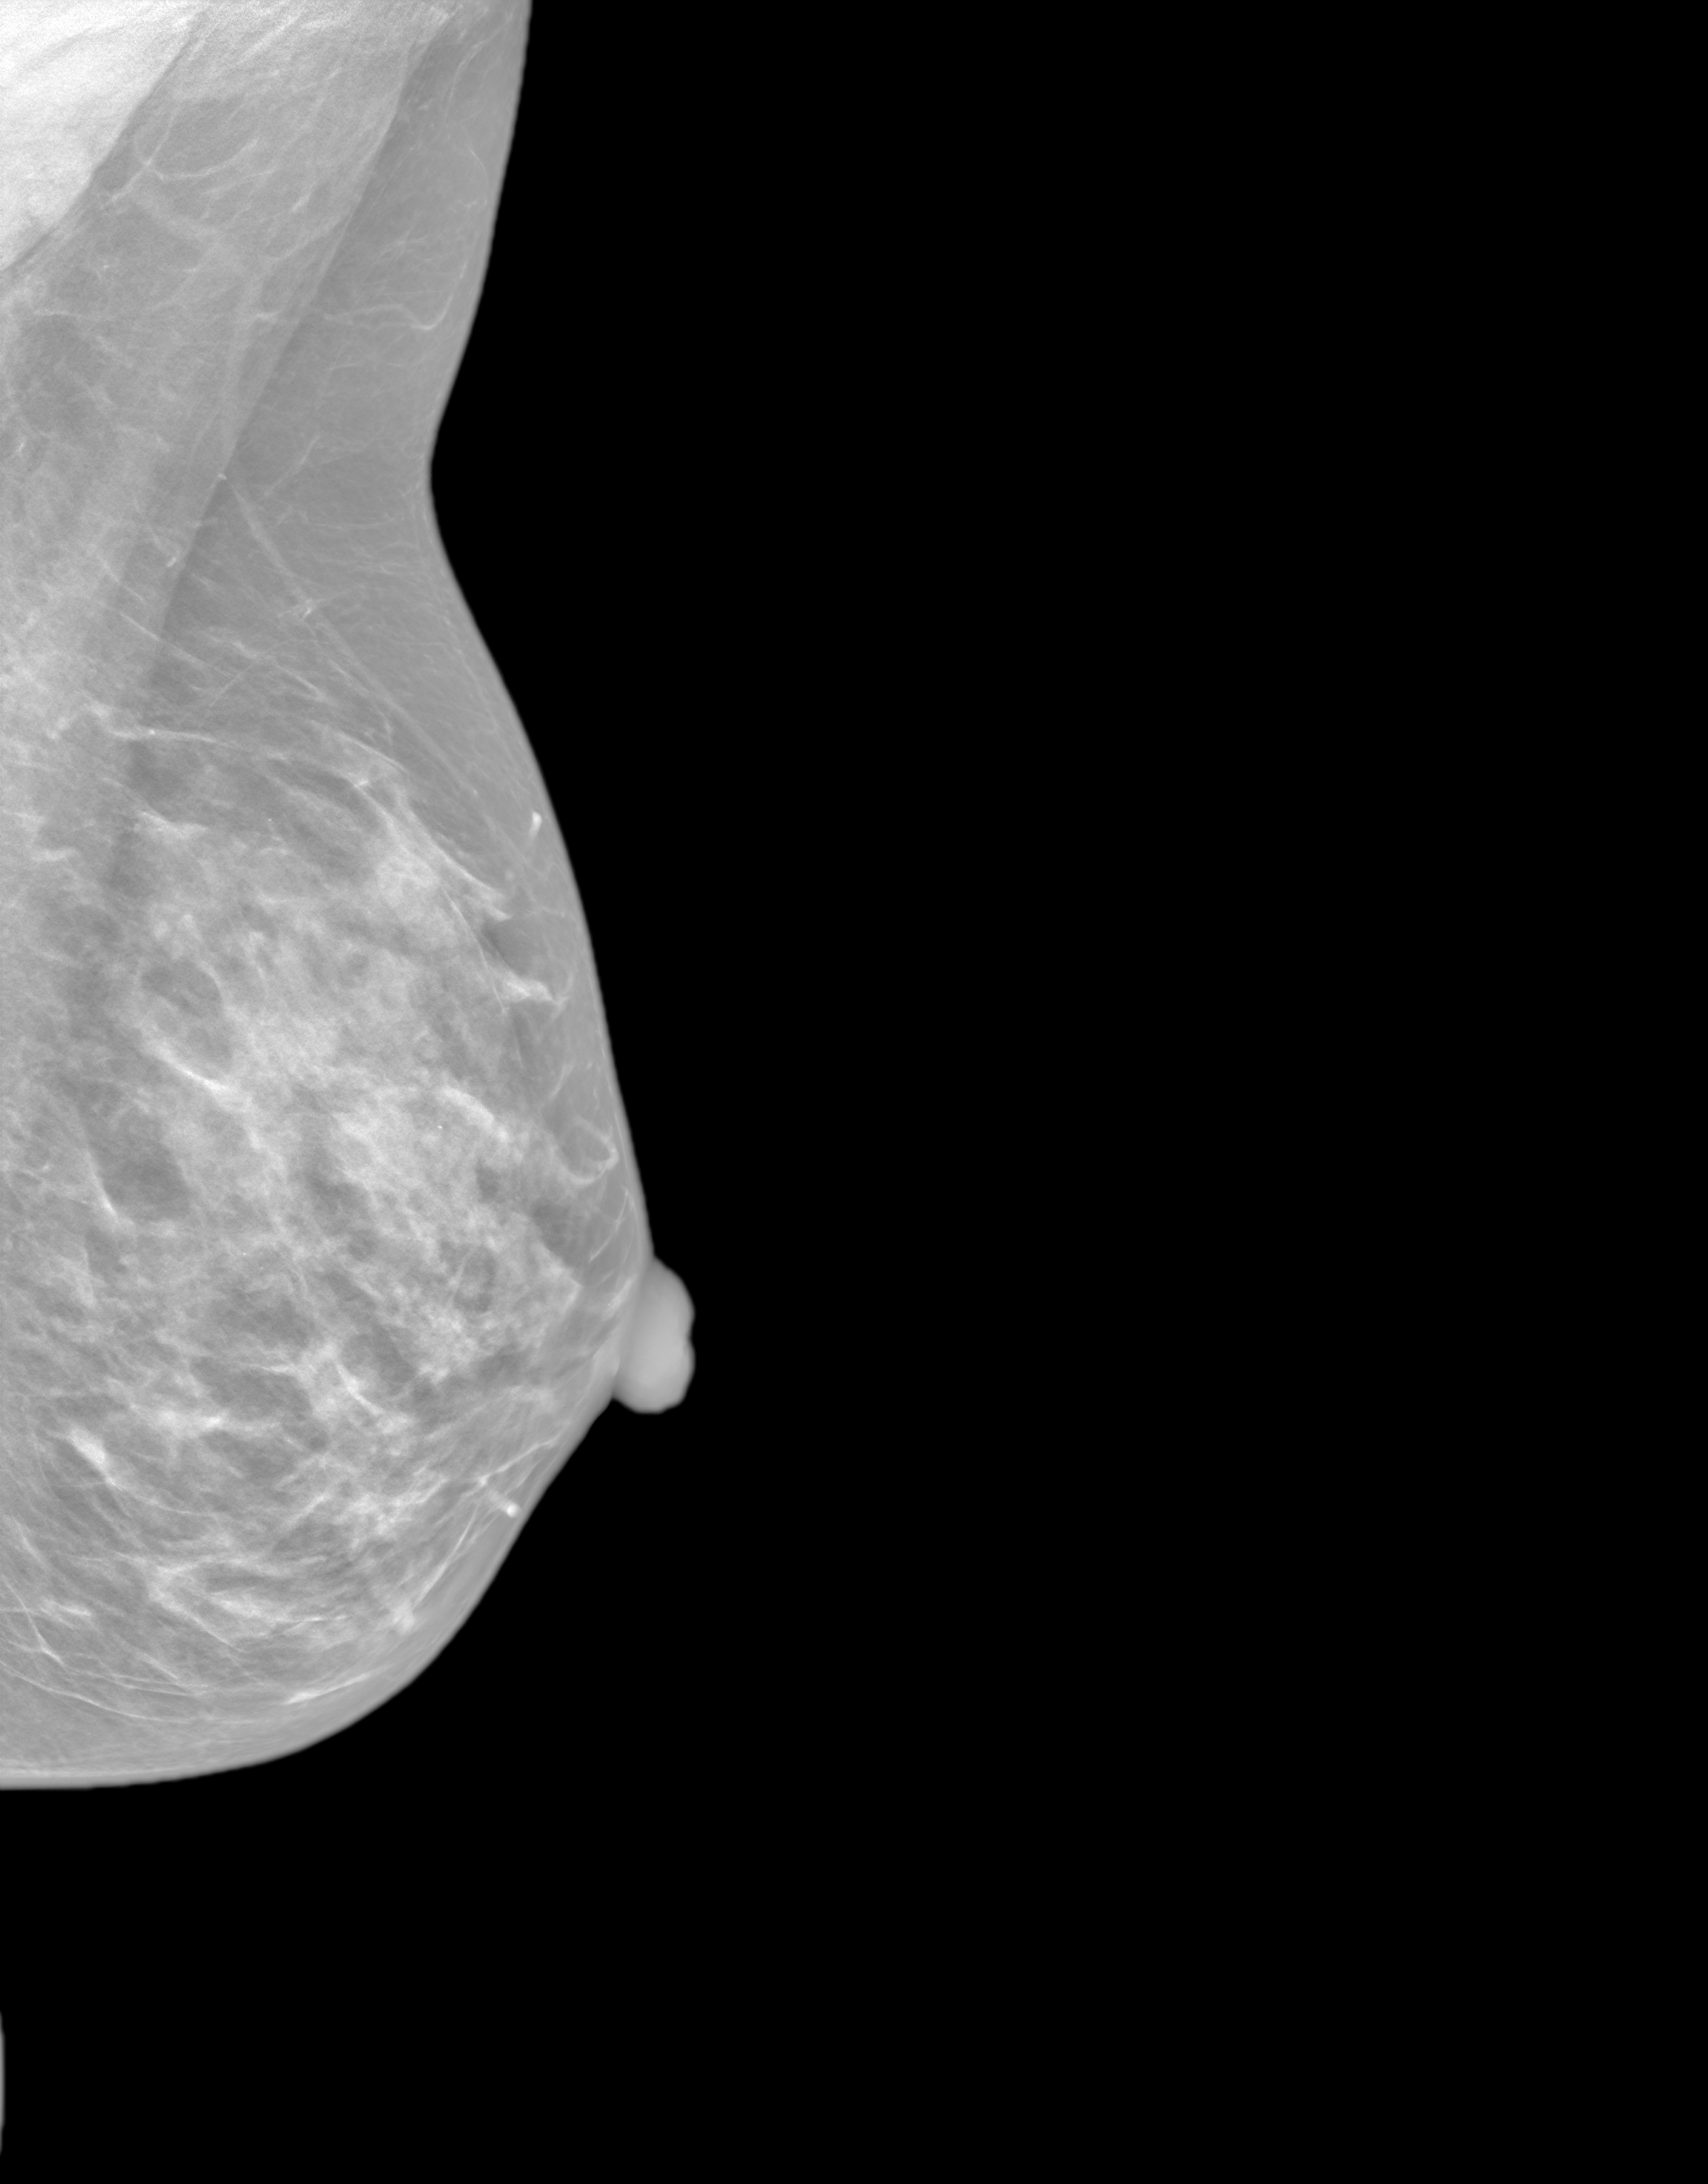
Screening examination. Female patient, age 43 years.
Image type: synthesized 2-D view from tomosynthesis. Breast: left. Projection: medio-lateral oblique projection.